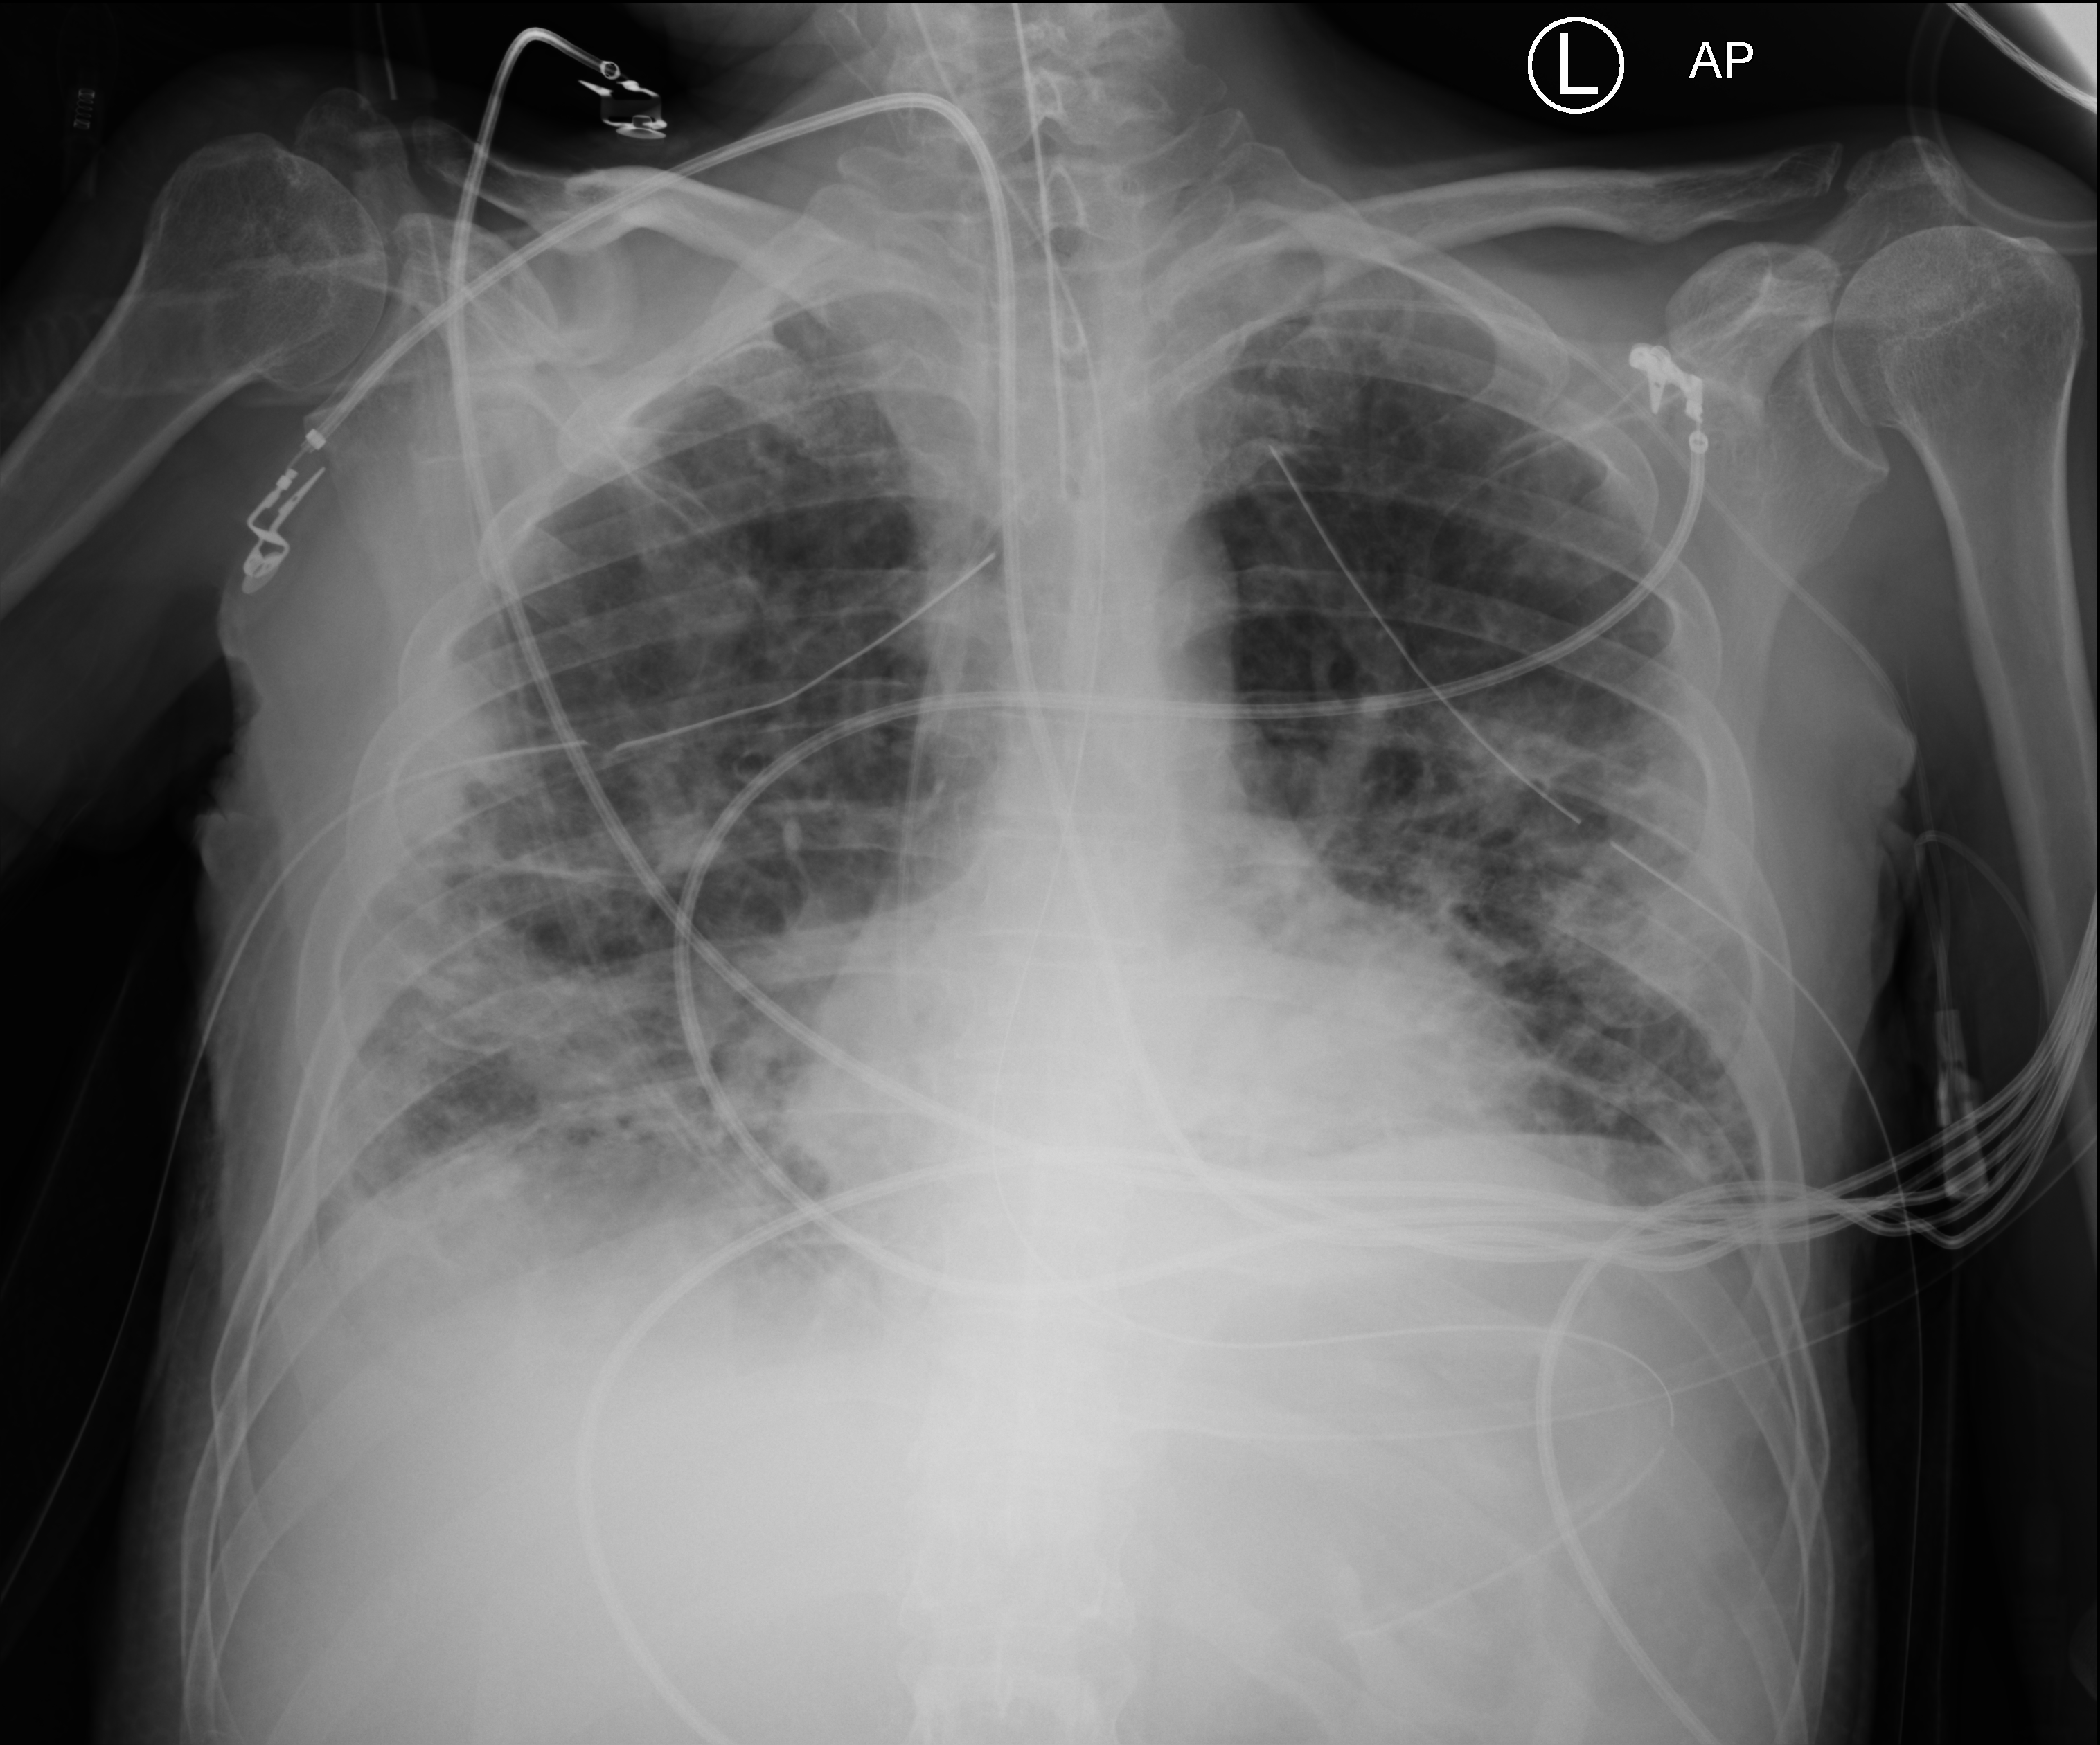
Chest X-ray (portable). Patient hospitalised with COVID-19; male, aged 18–59 years.
From the hospital-stay record, not from the radiograph (when in the stay this image was taken is not recorded): other chronic lung disease (admission record): no; COPD (admission record): no; admitted to intensive care during this hospital stay: yes.